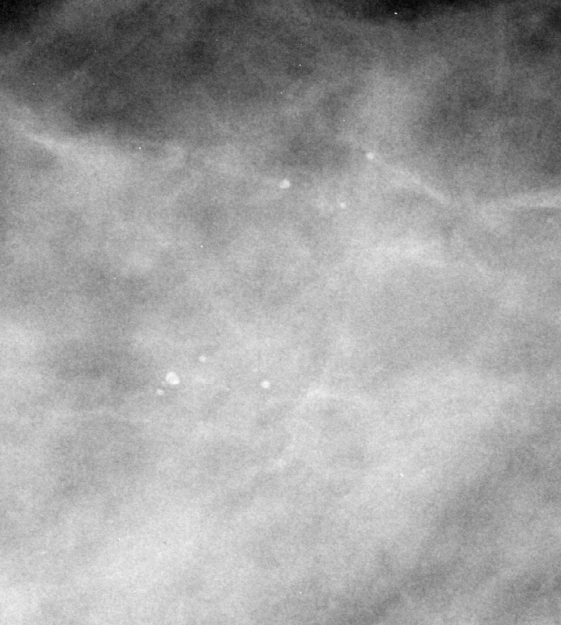
Crop from a digitized film mammogram around one marked abnormality; right breast; MLO view.
- Calcifications, morphology round and regular, distribution clustered; BI-RADS assessment category 4; pathology (as recorded): benign.